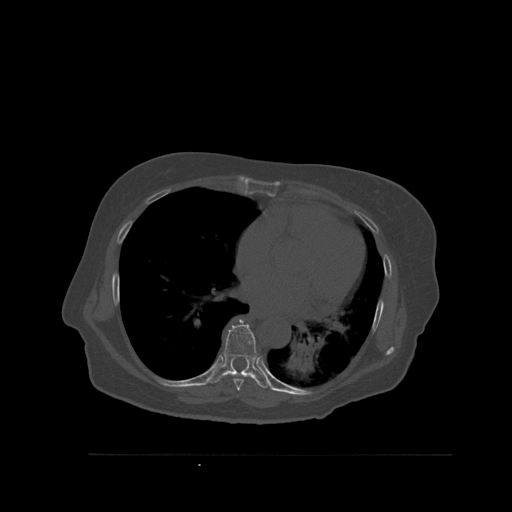
CT including the spine, one axial slice; position 355 of 527 along the scan axis; bone window (W 1800 / L 400 HU); 1.5 mm slice thickness; 512 × 512 image matrix, field of view 470 × 470 mm. Patient: female, 73 years. Case-level facts recorded for this patient, not image findings: primary cancer: breast.
Annotated regions visible in this slice (semi-automatically segmented with operator editing):
- T7 vertebra: bounding box [x1, y1, x2, y2] px = [231, 375, 257, 391]
- T8 vertebra: [209, 319, 269, 389]